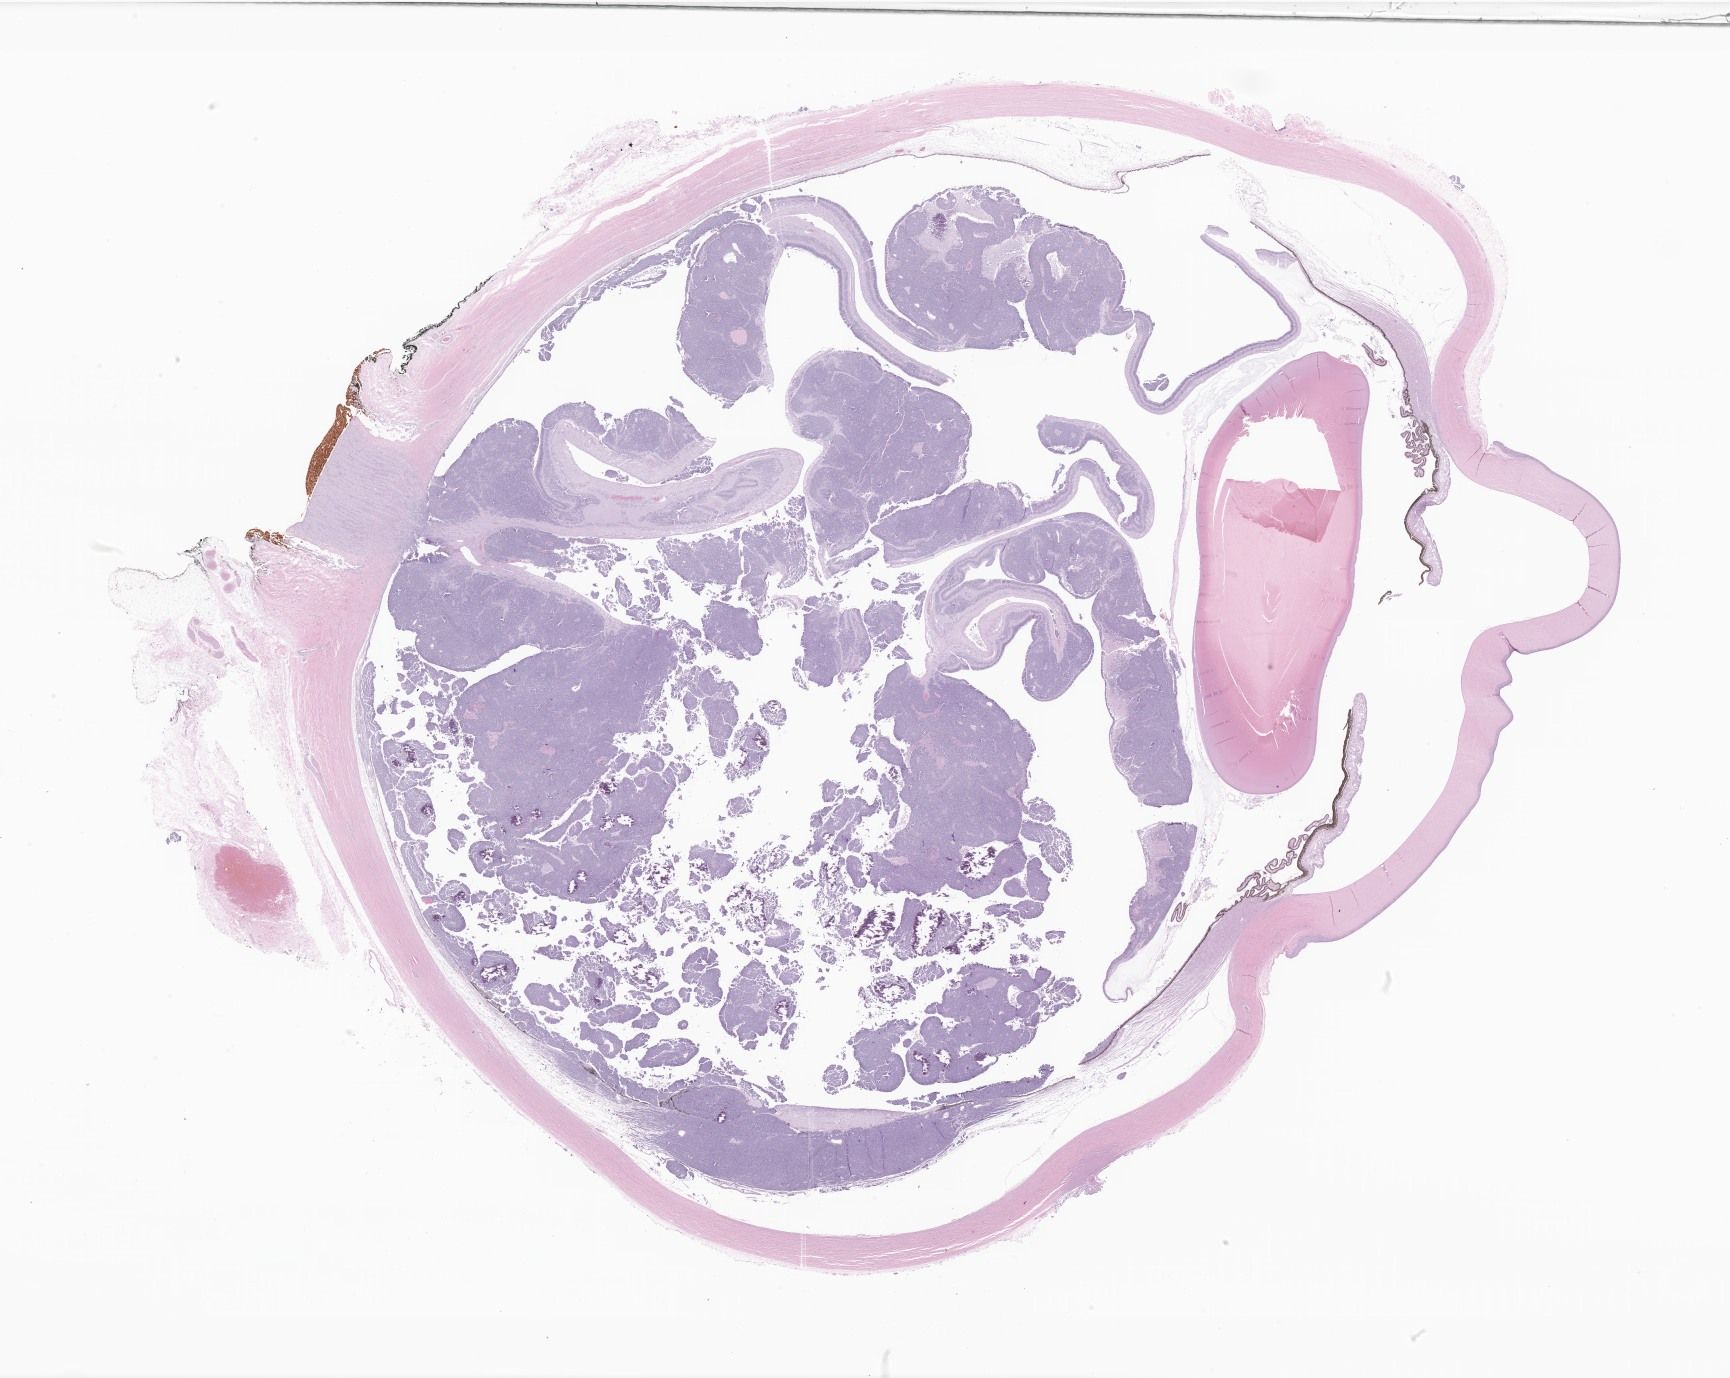
Digitized H&E-stained section of tumor tissue from the retina, whole scanned area (about 29.2 x 23.2 mm) shown as a low-resolution overview; FFPE section. Patient: male, age 465 days (about 1.3 years).
Recorded diagnosis: Retinoblastoma, NOS.